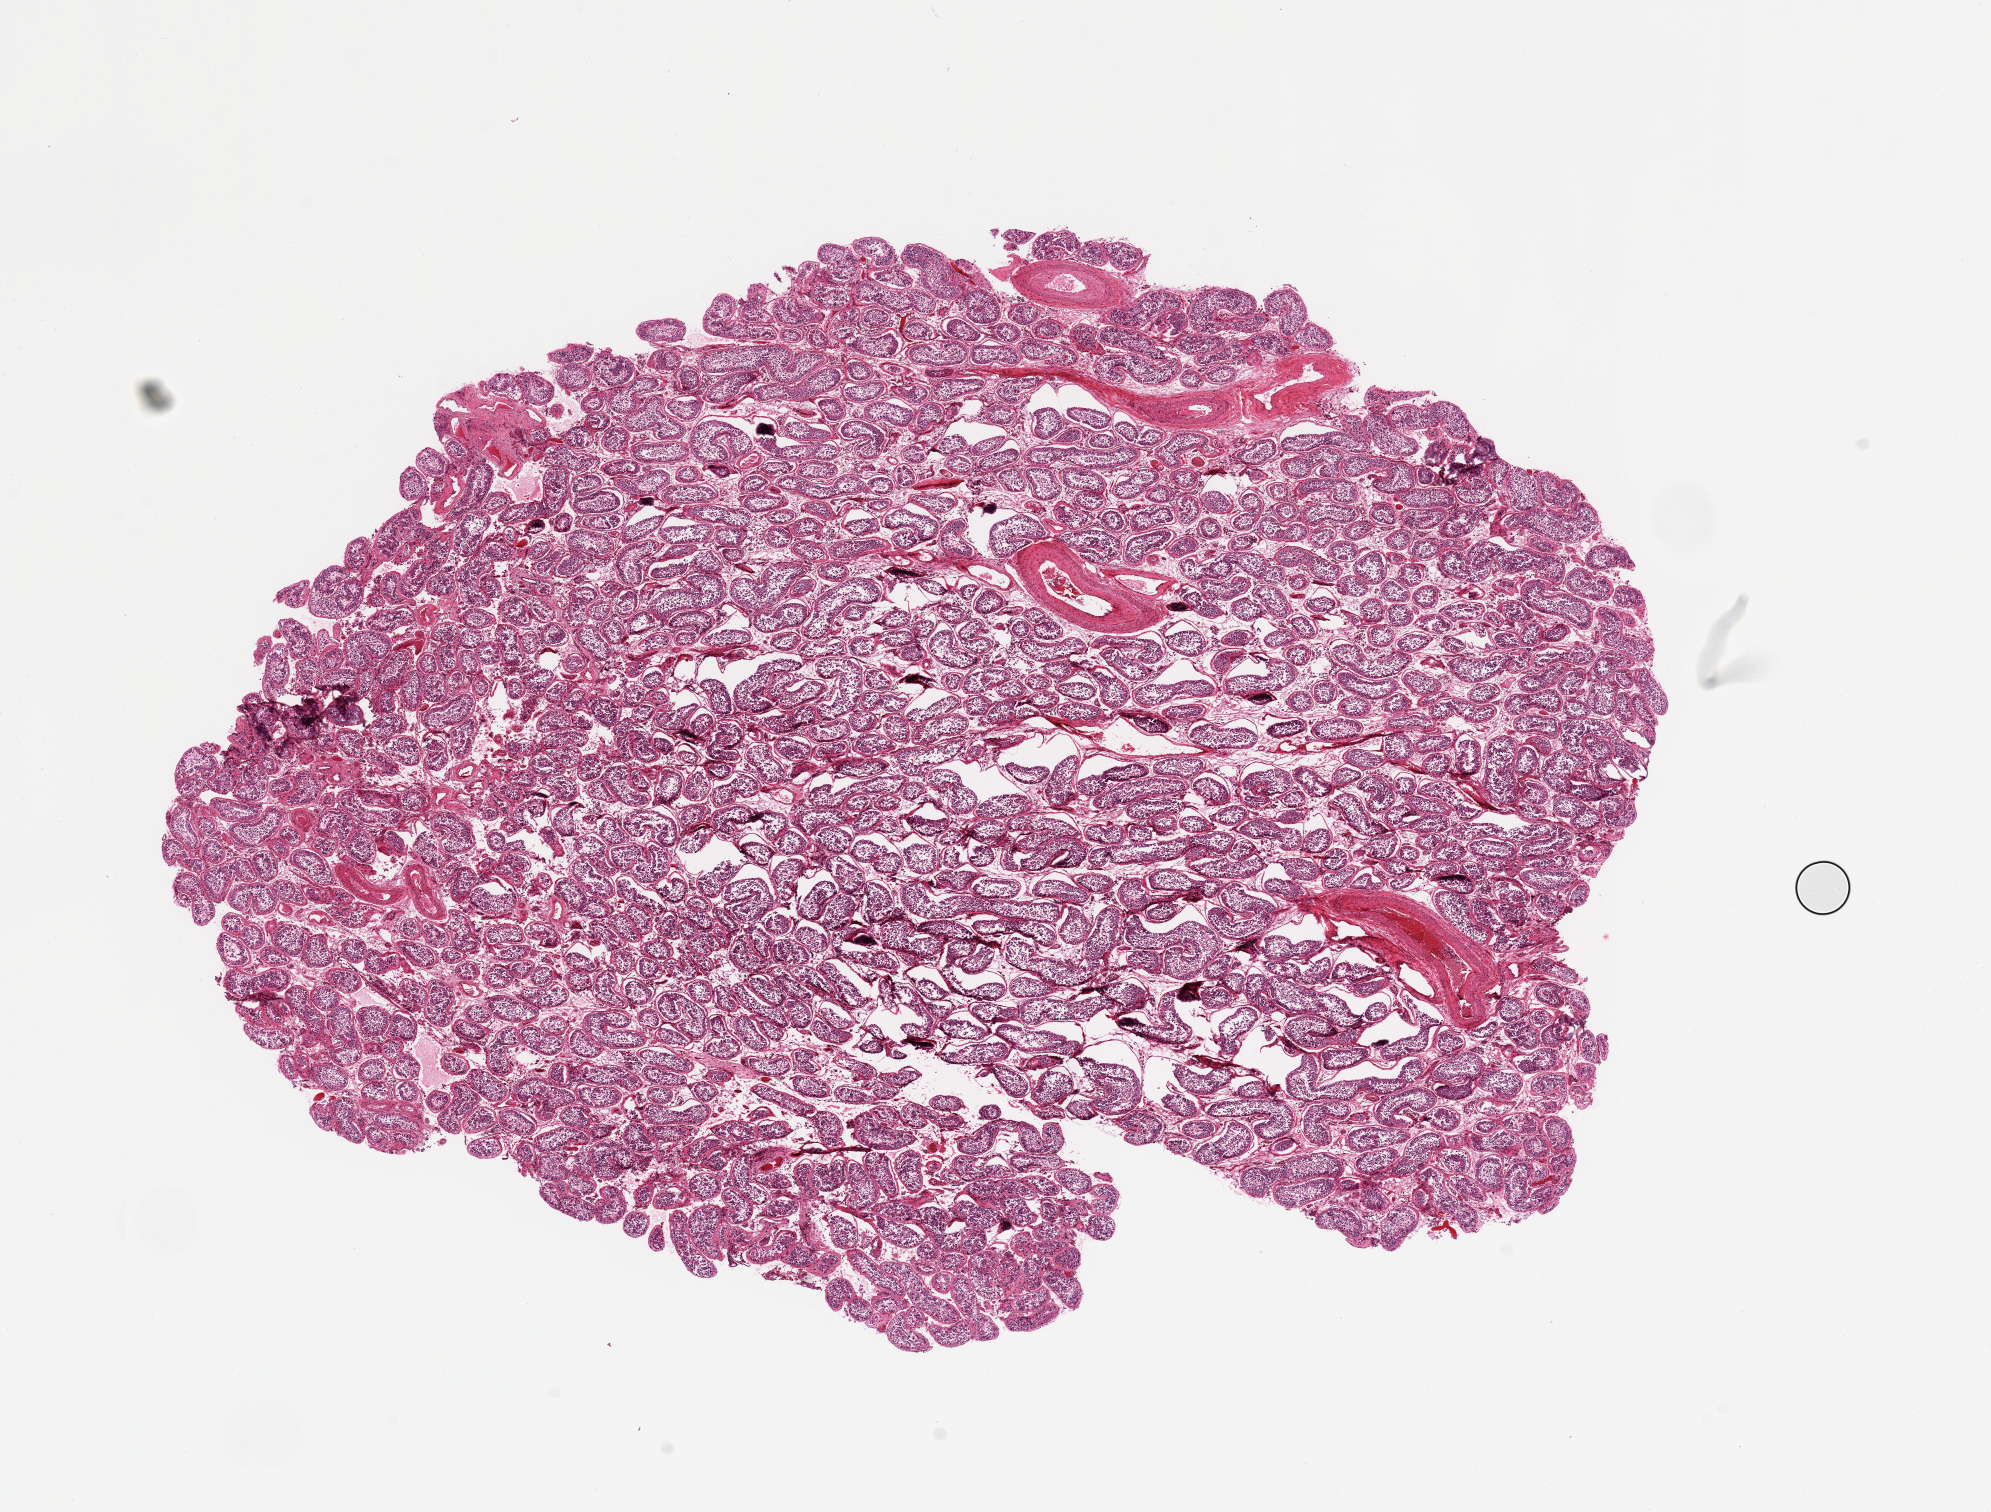
Haematoxylin and eosin whole-slide image — whole scanned area (about 15.8 x 12.0 mm) shown as a low-resolution overview, PAXgene-fixed paraffin-embedded (PFPE) section, target tissue: testis, tissue donor sample. Male donor.
Review note (as recorded): ~50% autolyzed.